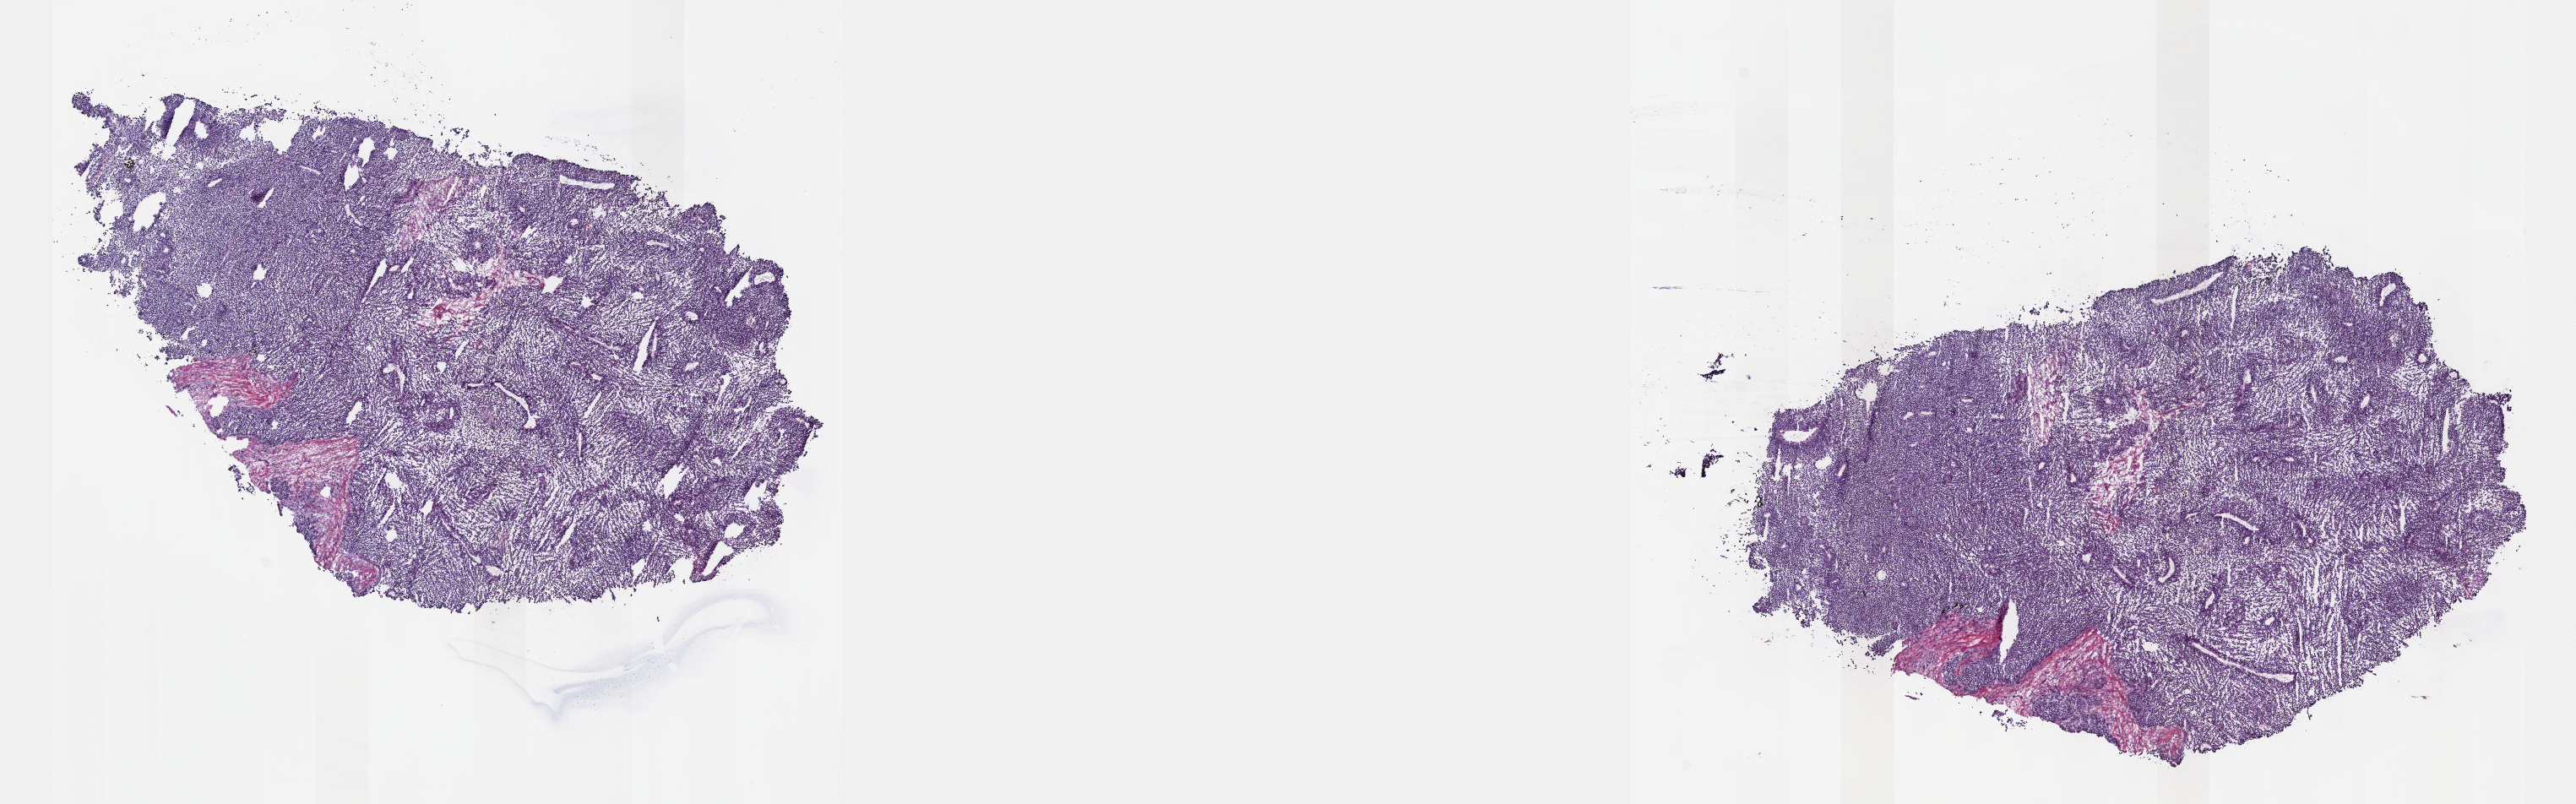
H&E whole-slide image — whole scanned area (about 24.6 x 7.7 mm) shown as a low-resolution overview. Frozen section from the top of the tissue portion. Metastatic tumour sample, sampled site: connective, subcutaneous and other soft tissues of trunk. Female patient; age at initial diagnosis 63 years. Composition of this section per pathologist review: tumour cells 90%, tumour nuclei 90%, normal cells 0%, stromal cells 10%, necrosis 0%. Inflammatory infiltration, as recorded: lymphocyte infiltration 0%, monocyte infiltration 0%, neutrophil infiltration 0%.
This section: metastatic tumour tissue. Patient diagnosis: Malignant melanoma, NOS.